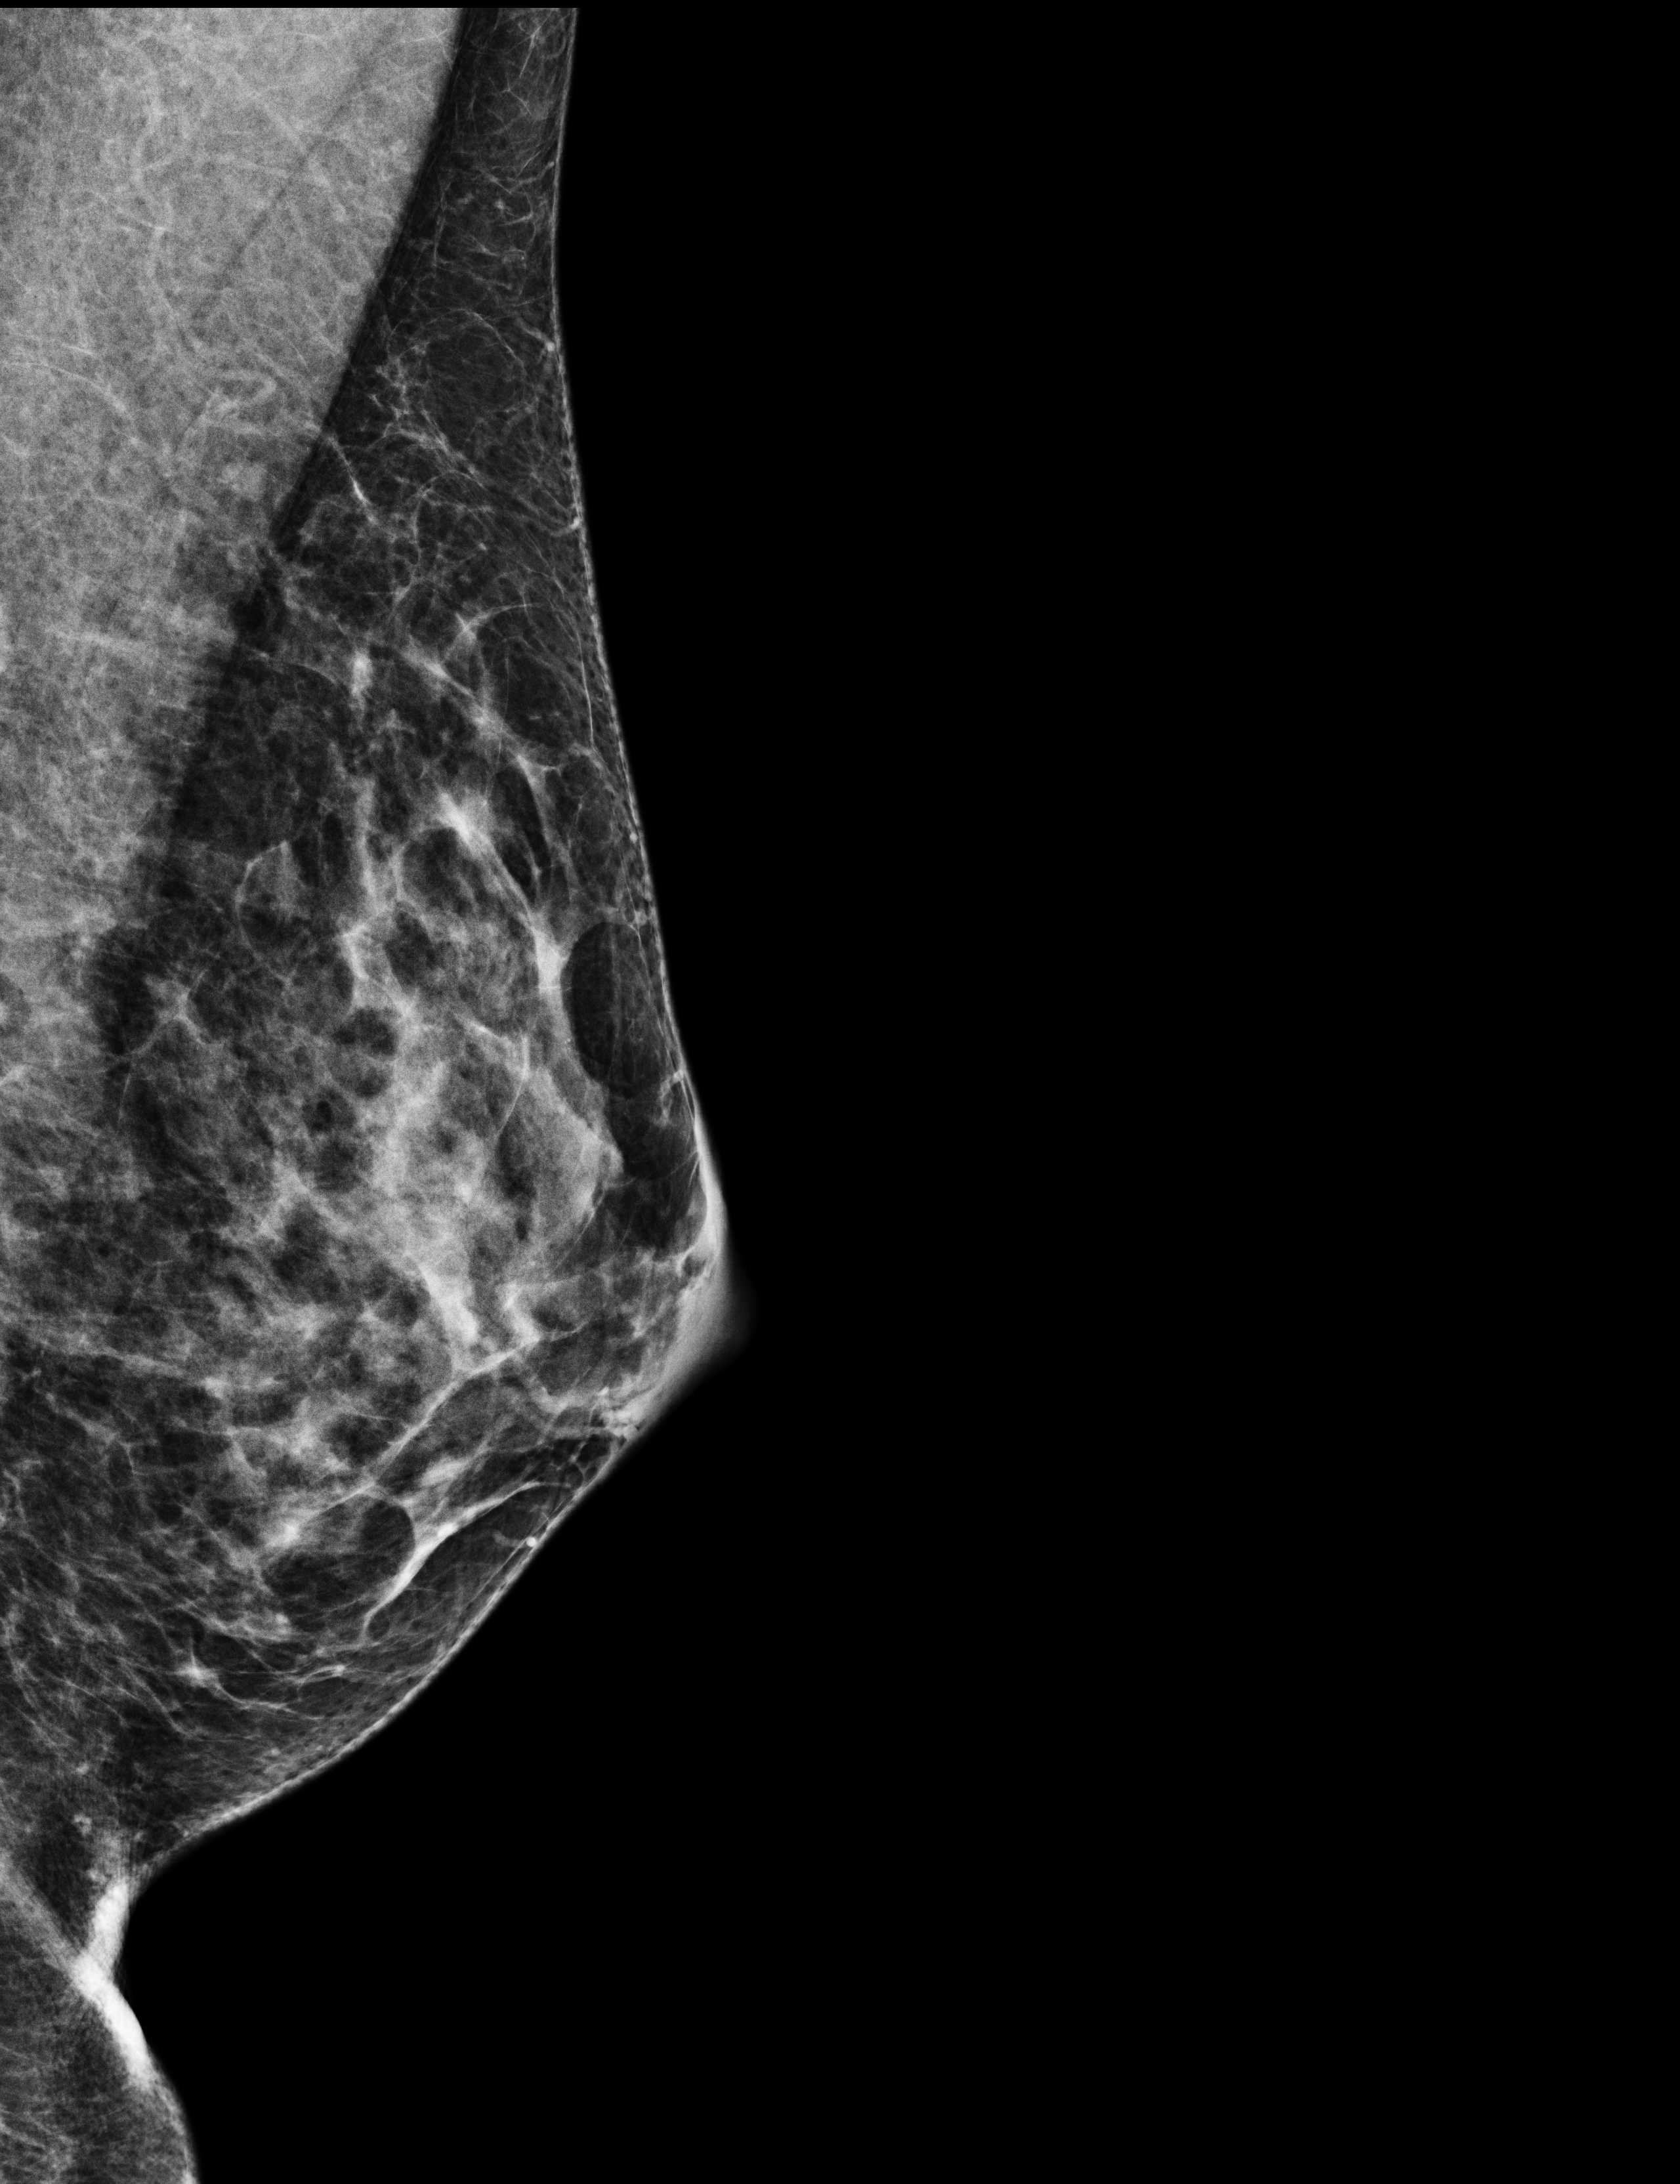
Digital mammogram (FFDM), left breast, mediolateral oblique (MLO) view, annual screening mammography examination, compressed breast thickness 44 mm. Patient aged 51 years (female).
Breast density at the screening exam (both breasts): heterogeneously dense (BI-RADS density category c). Final BI-RADS category for the screening round (tomosynthesis exam, both breasts): category 1. Recall: no recall after this screen.